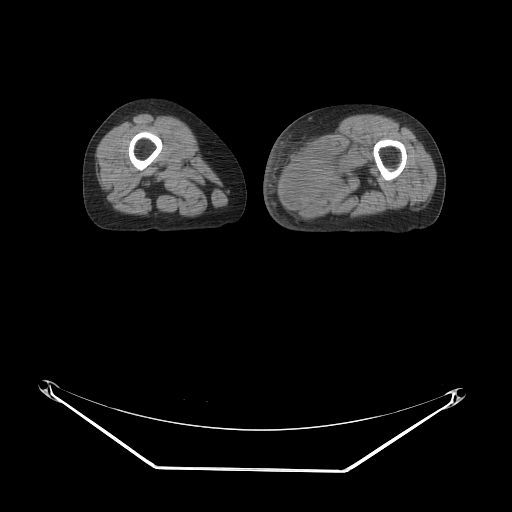
CT of an extremity soft-tissue mass (from a PET/CT study), one axial slice. Slice 20 of 91 in the series (ordered by position). 140 kVp. Soft-tissue window (W 400 / L 40 HU). 3.75 mm slice thickness. 512 × 512 image matrix, field of view 500 × 500 mm. Female patient. From the clinical record (not read from this slice): histological type: pleomorphic leiomyosarcoma; grade: high; site of the primary tumour: left thigh.
Outlined on this slice (expert contour drawn on MRI and transferred to this co-registered scan by the dataset authors):
- gross tumour volume including surrounding oedema: bounding box (x1, y1, x2, y2) in pixels: (281, 132, 366, 209)
- gross tumour volume (mass): (281, 153, 346, 207)